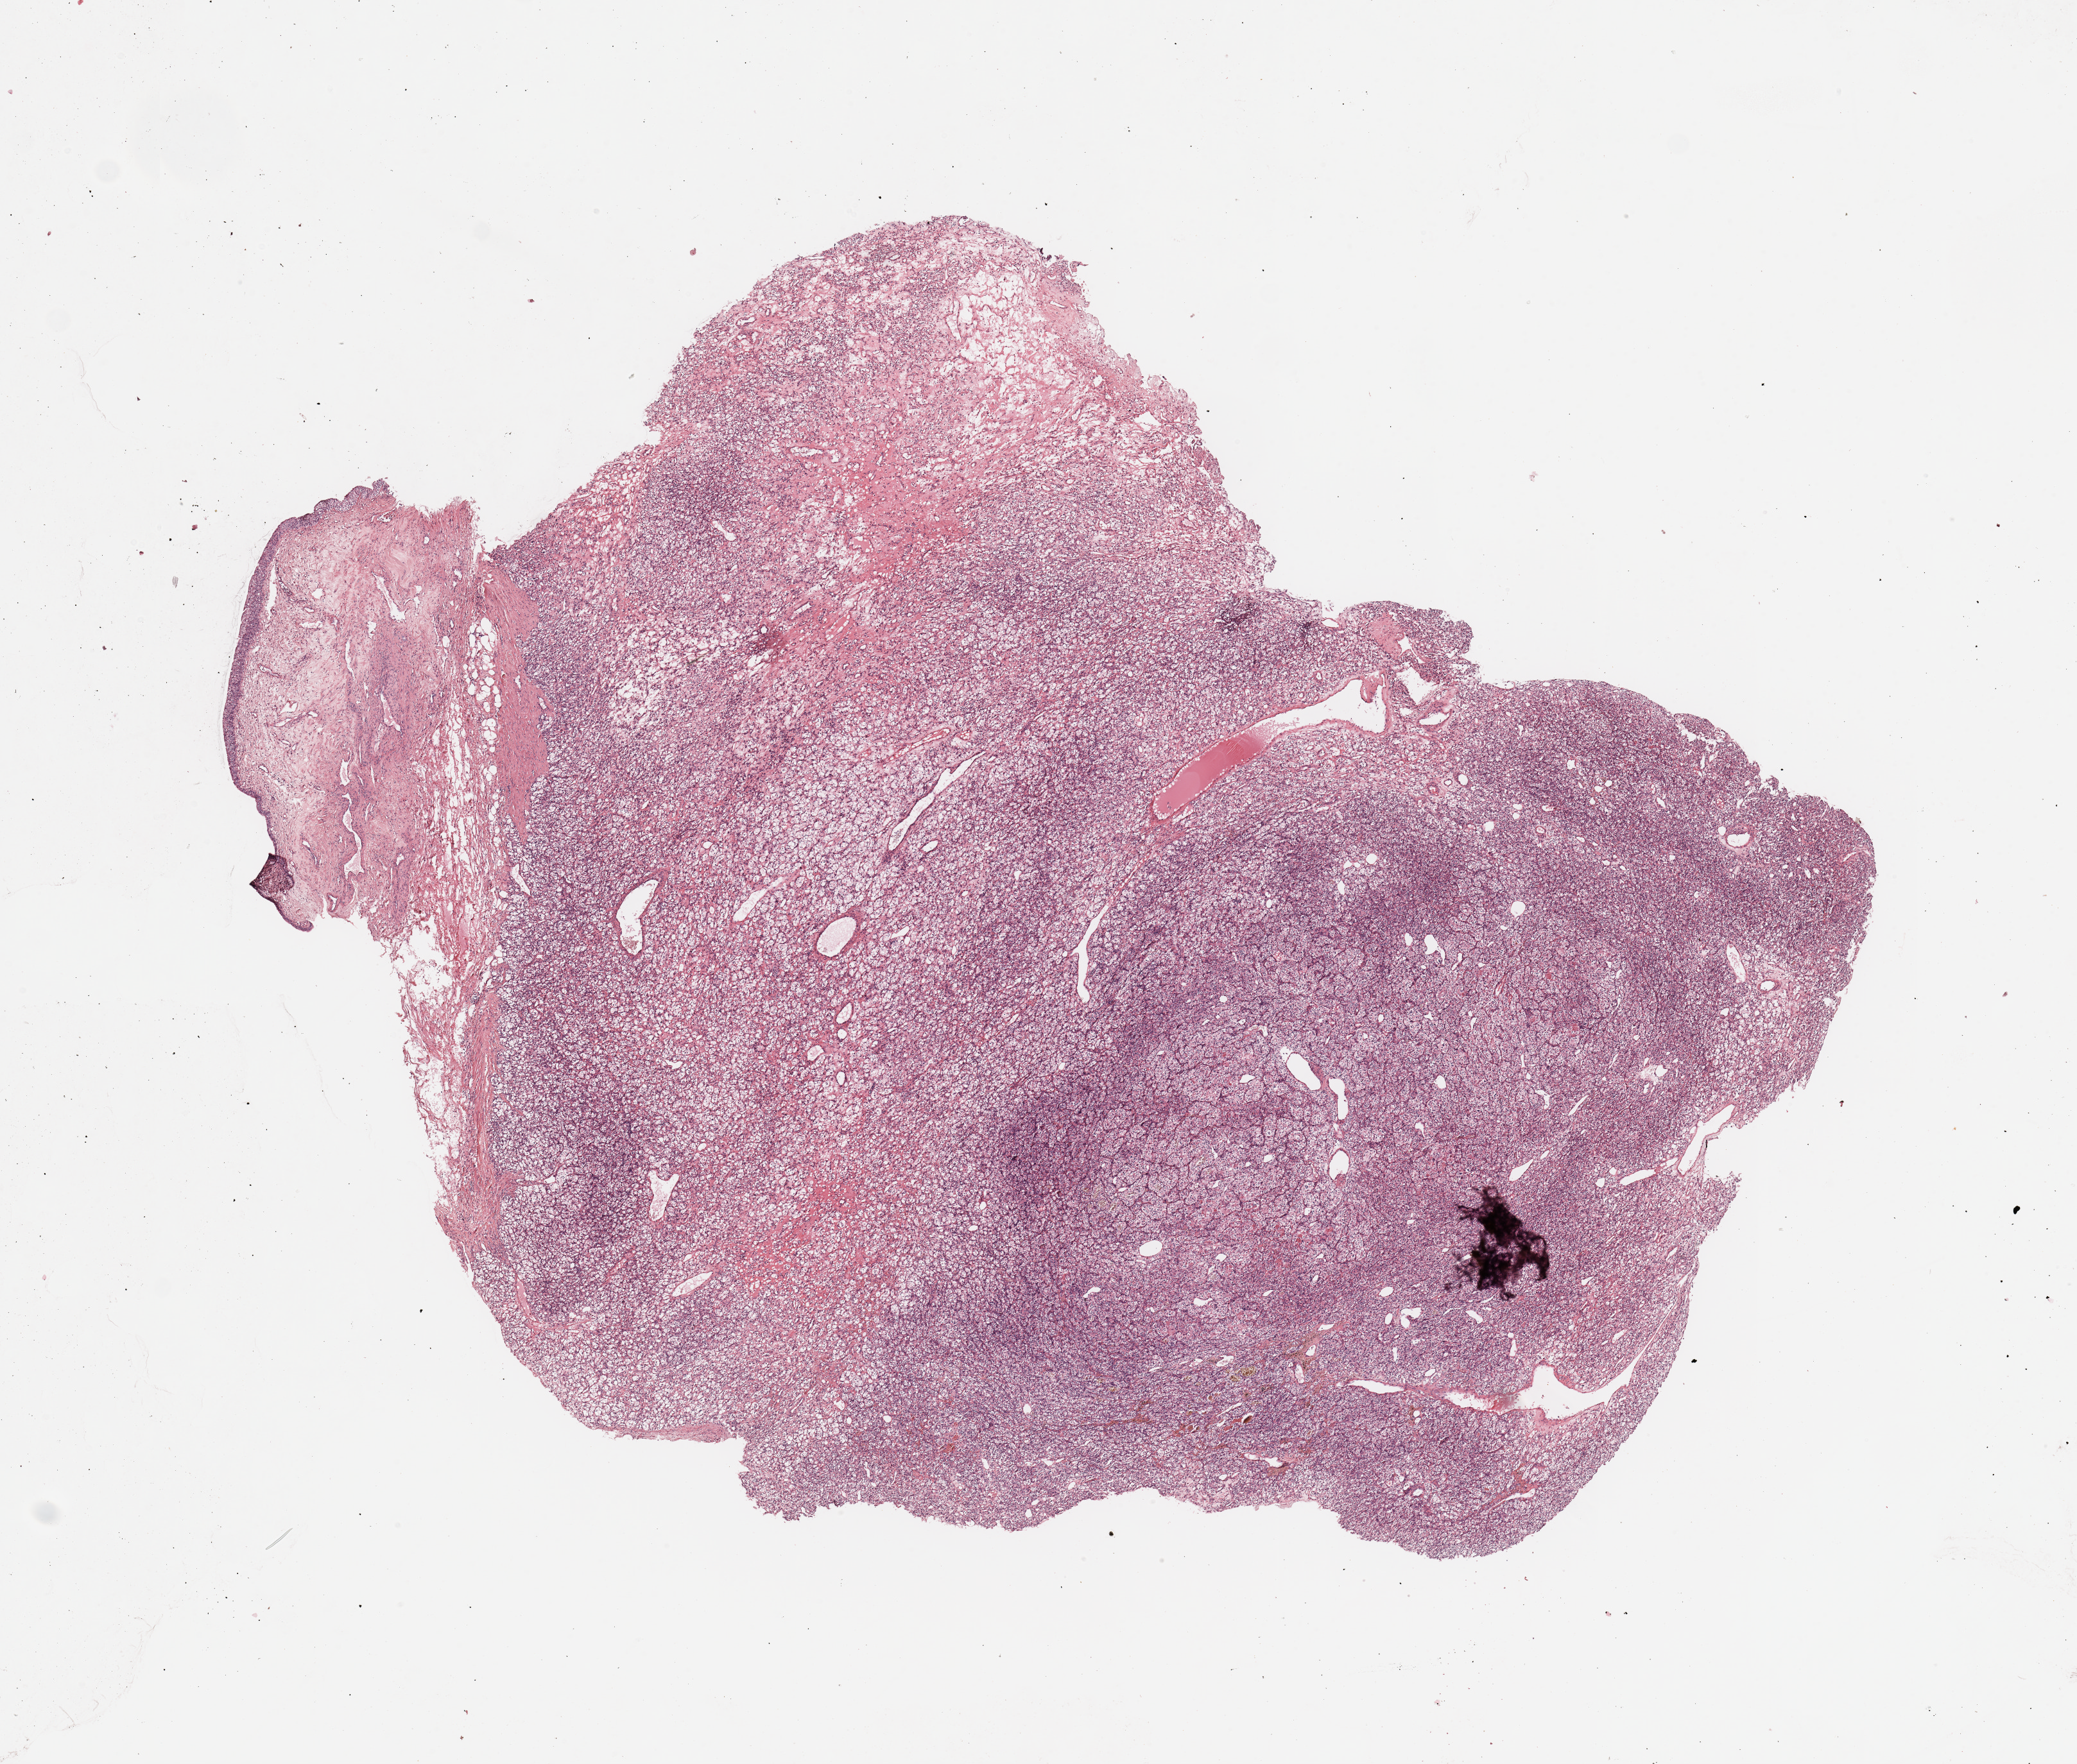
H&E whole-slide image — a low-resolution overview of the entire scanned area, about 12.8 x 10.9 mm (slide scanned at 20x). Tumour tissue sample, sampled site: kidney. Female, 66 y/o. Histologic grade: G2 (moderately differentiated). Slide review estimates, as recorded: tumour nuclei 85%, necrosis 5%.
• AJCC pathologic stage: III
• diagnosis: Renal cell carcinoma, NOS
• primary tumour site (as recorded): upper pole